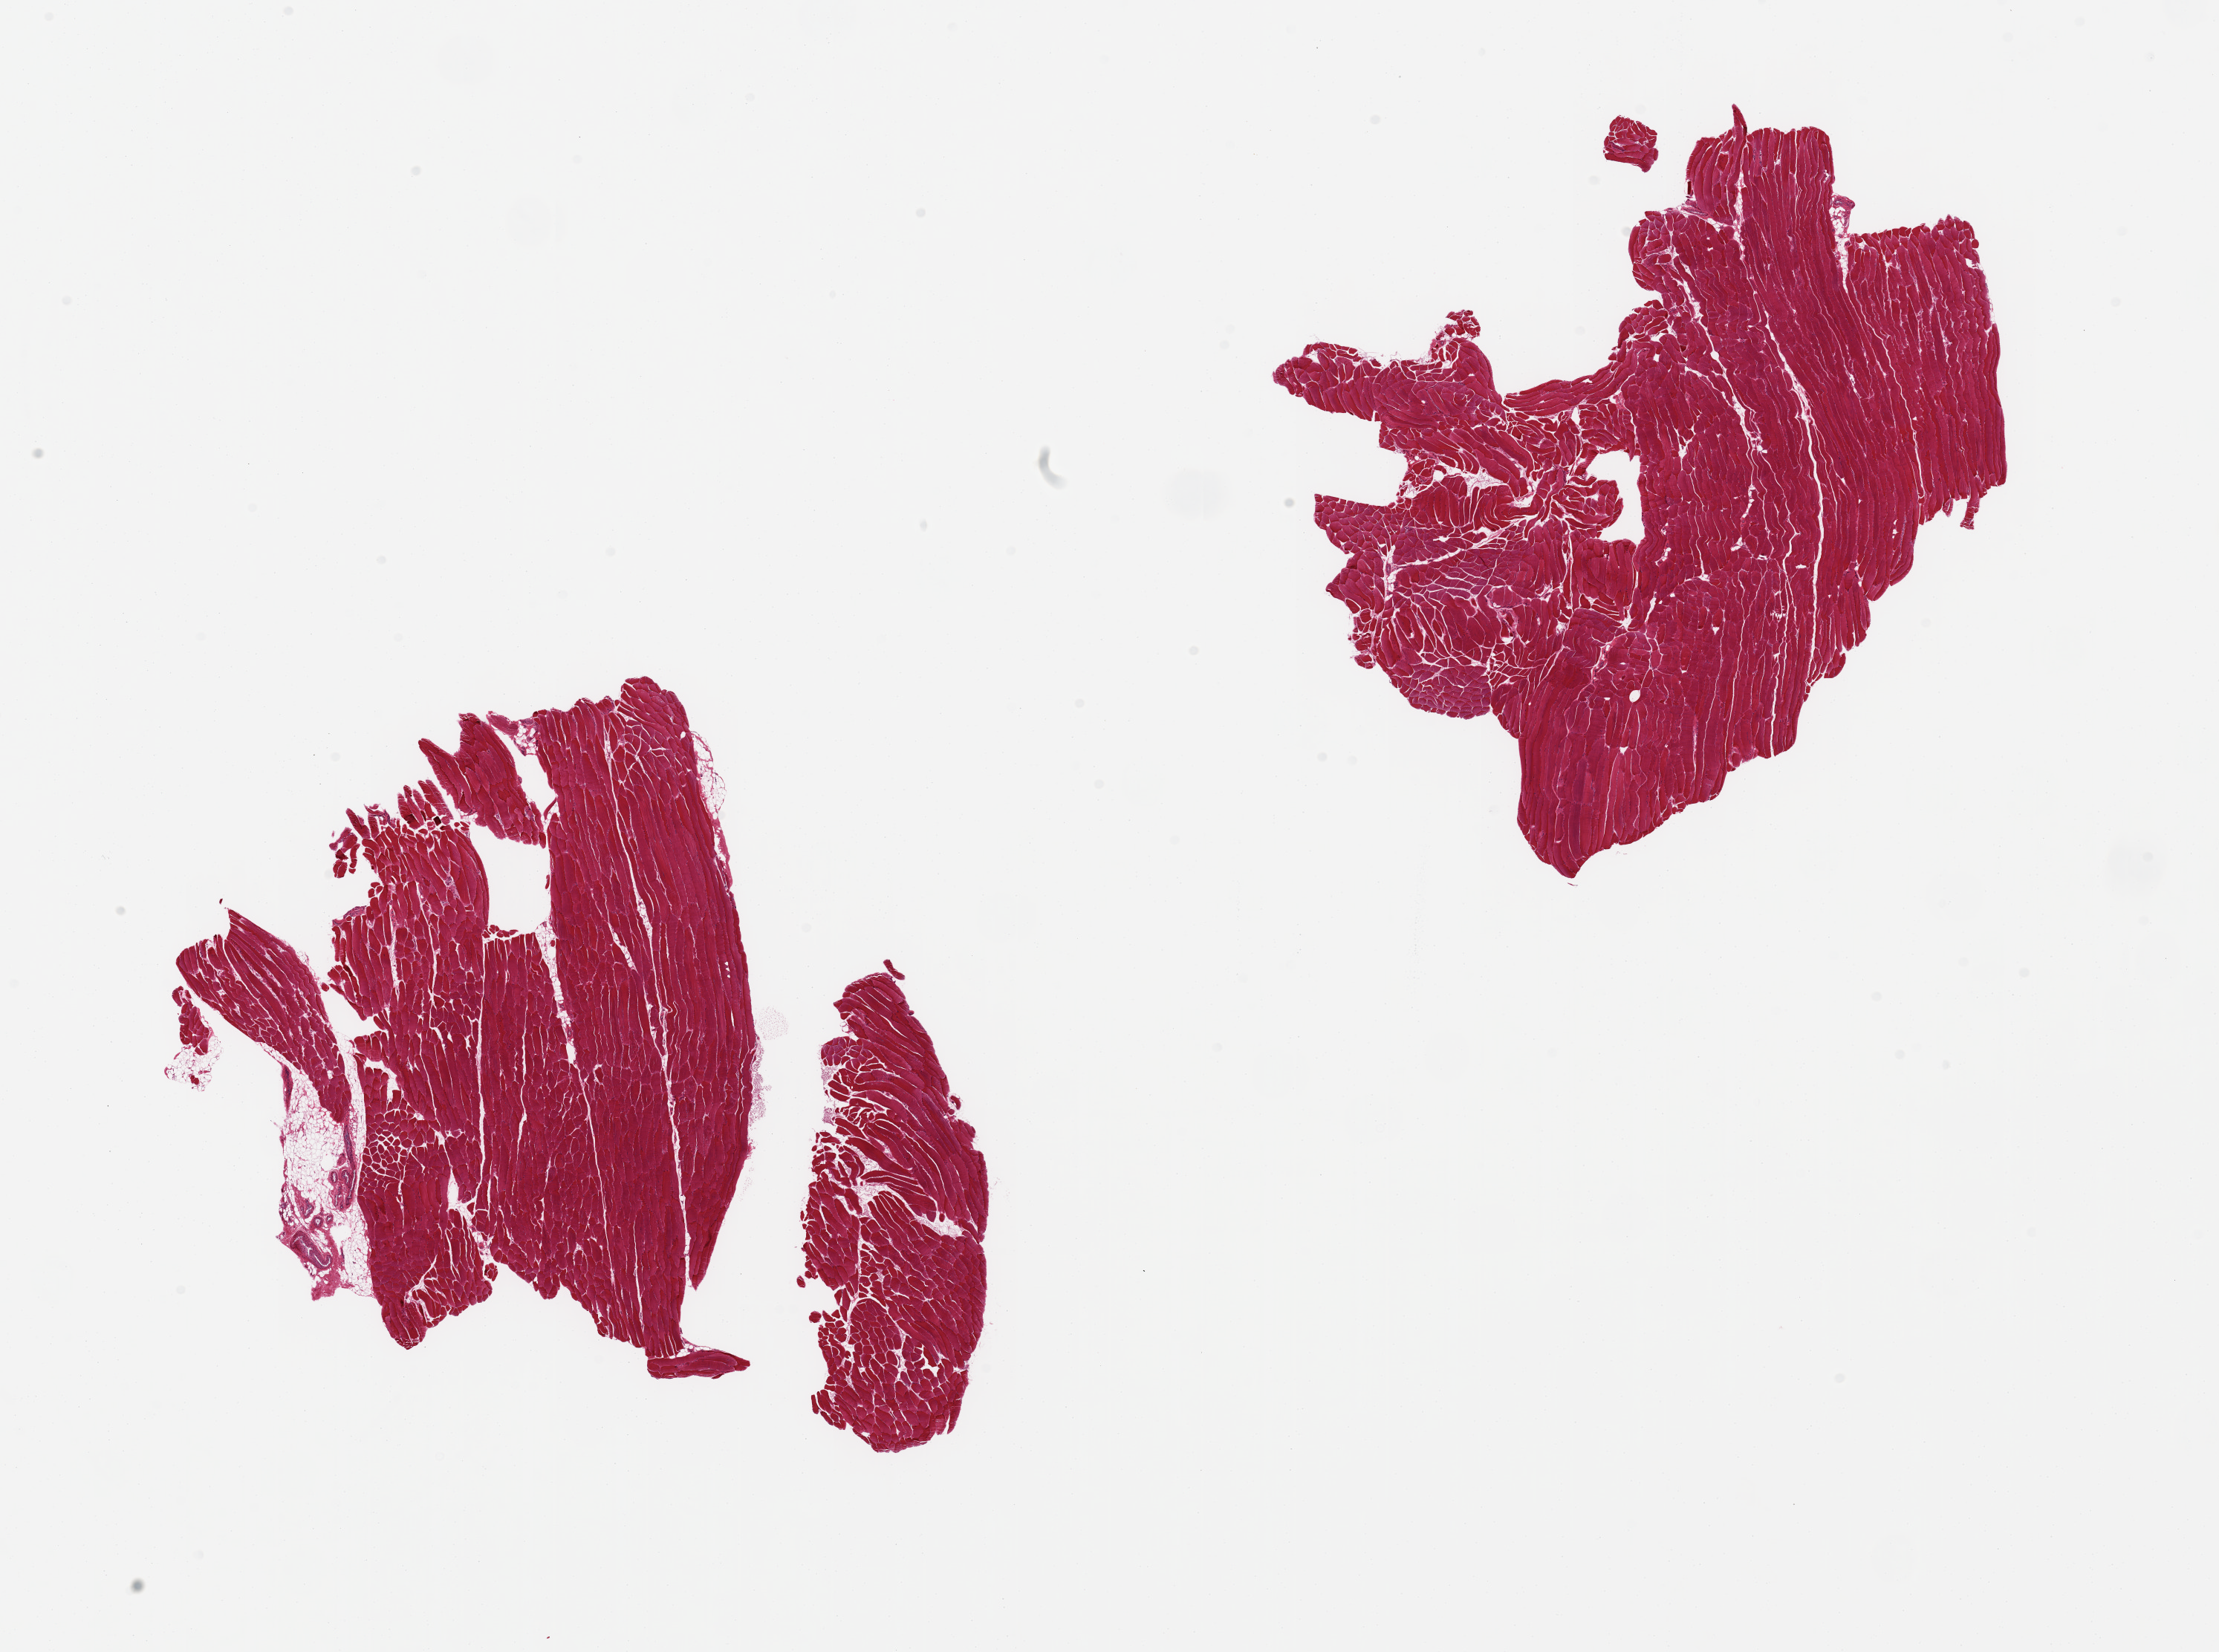
H&E whole-slide image — whole scanned area (about 23.6 x 17.6 mm) shown as a low-resolution overview, PAXgene-fixed paraffin-embedded (PFPE) section, target tissue: skeletal muscle, tissue donor sample.
Review note (as recorded): 2 pieces; 5% internal fat in 1 piece.